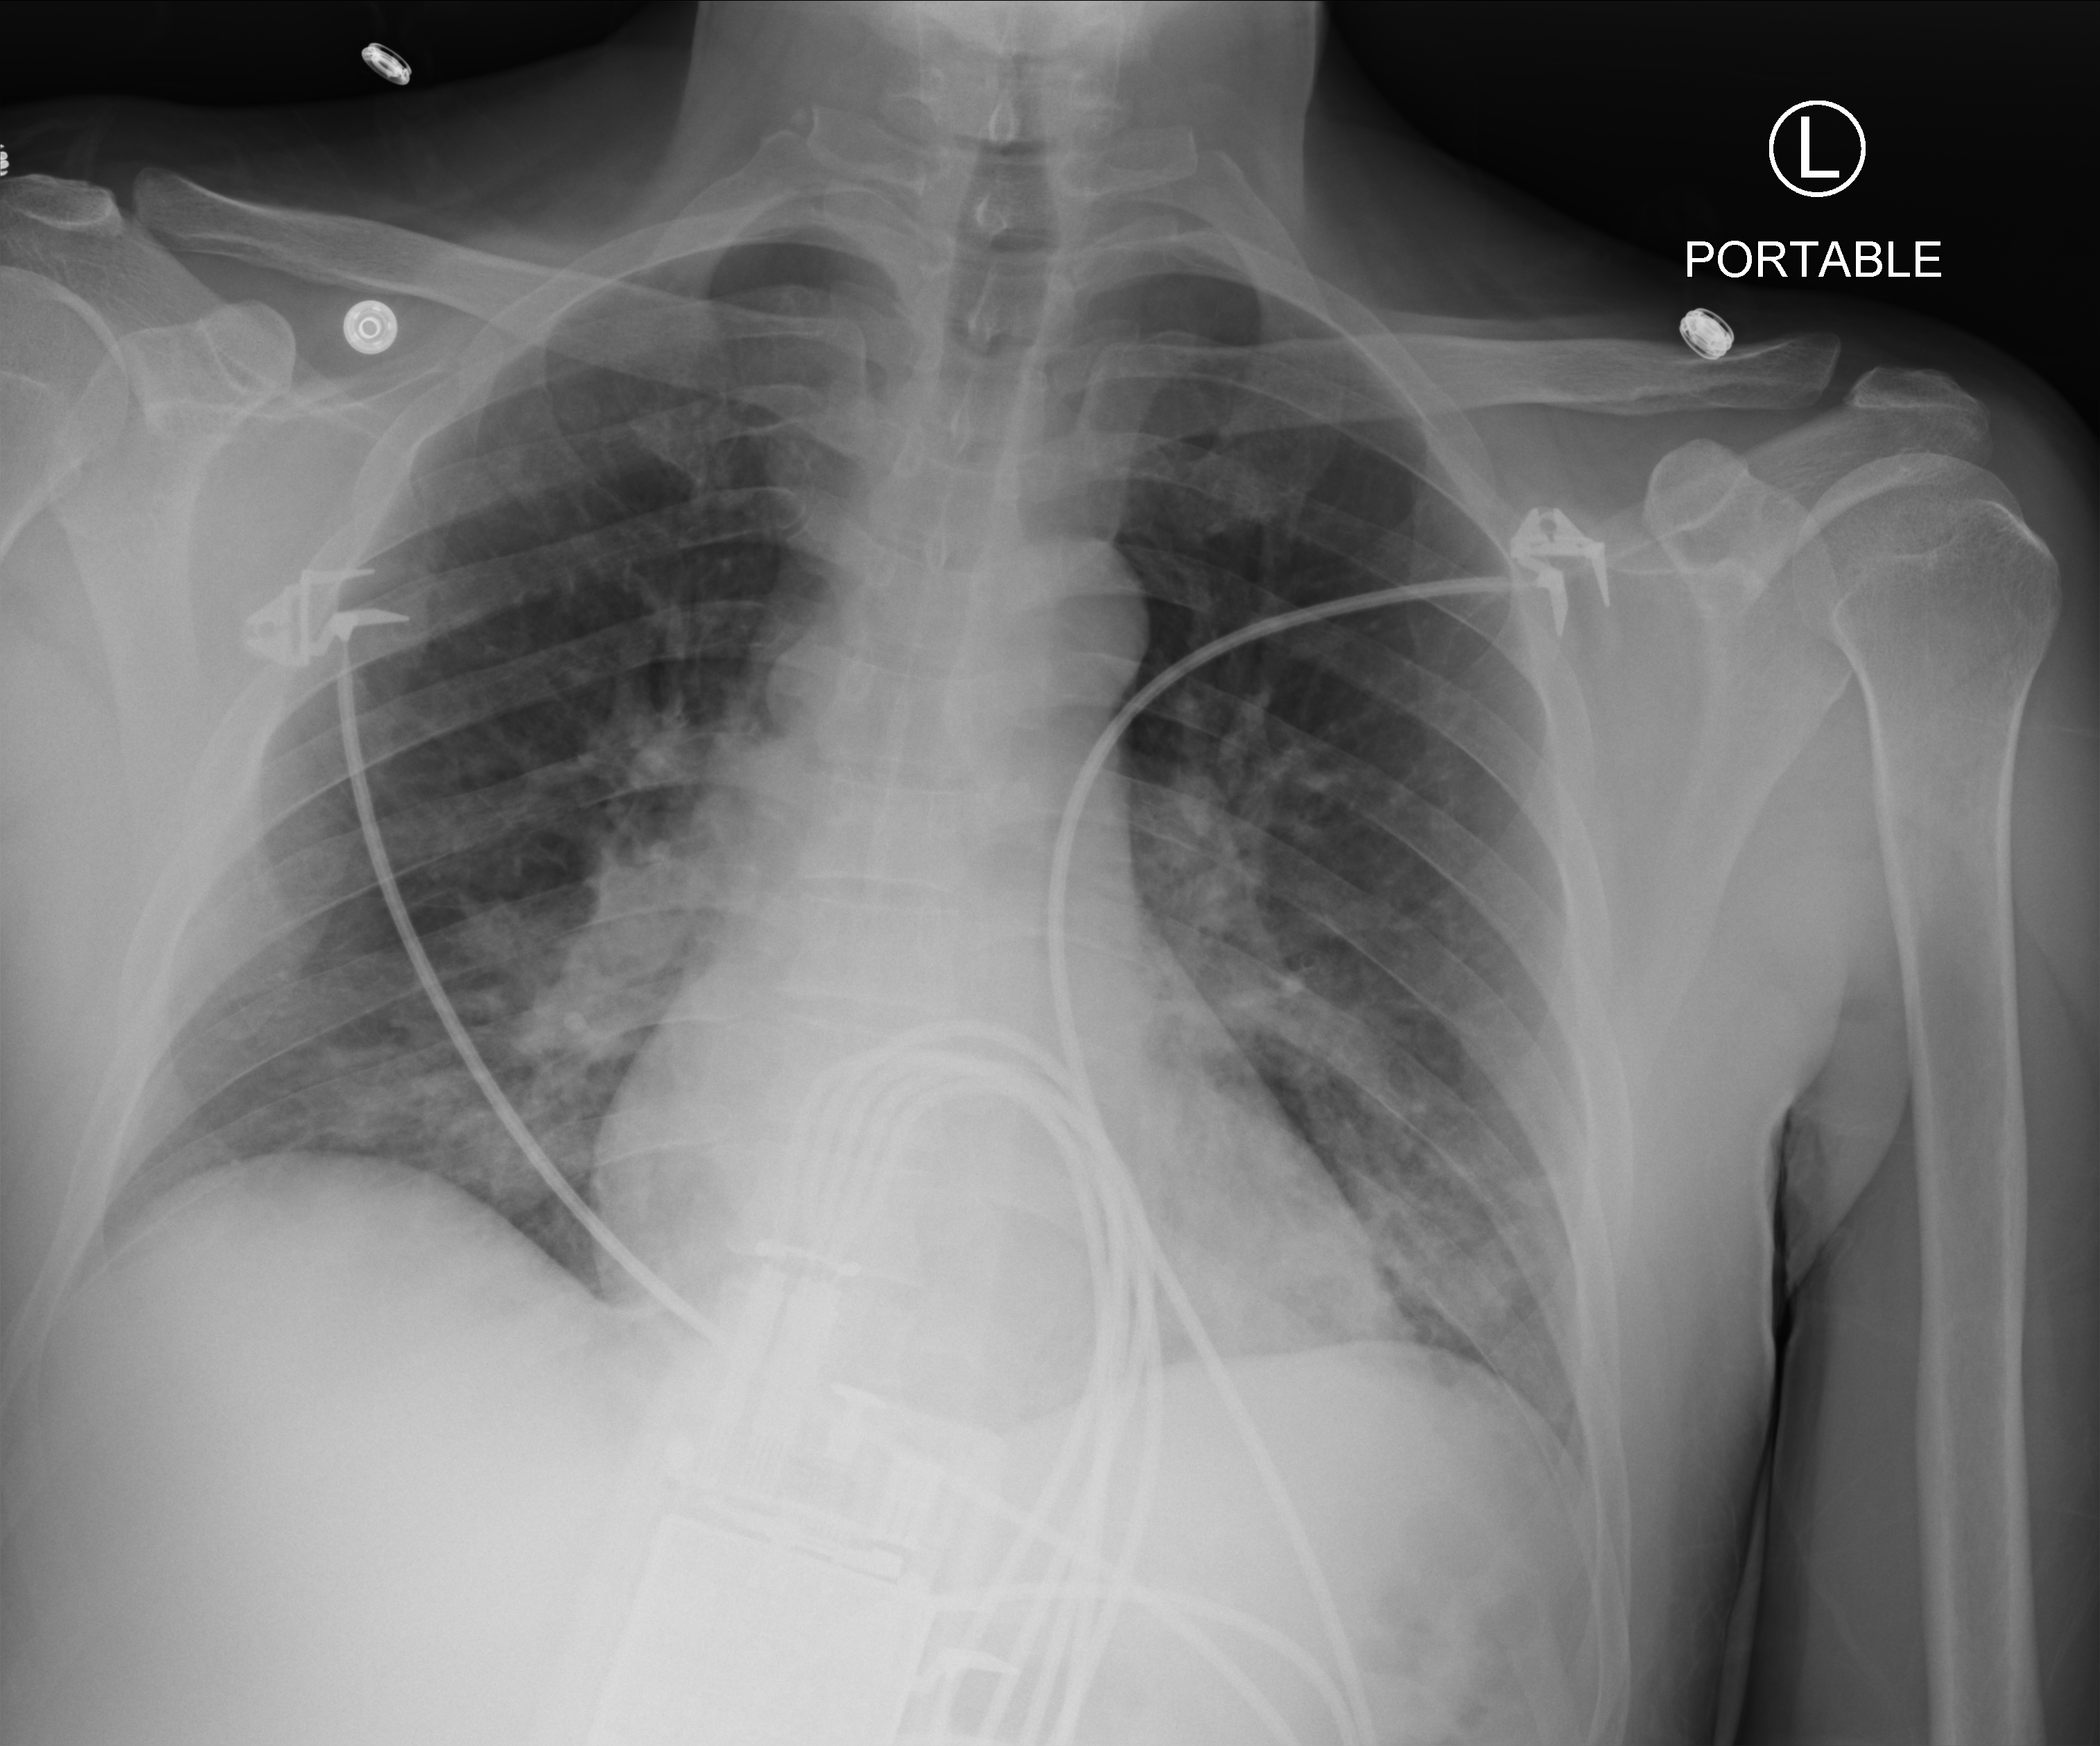
Bedside chest radiograph (computed radiography), anteroposterior (AP) projection. Male patient hospitalised with COVID-19, age 18–59 years.
Admission-level facts for this patient (not findings on this image; timing relative to this image not recorded): length of hospital stay: 11 days; mechanically ventilated during this hospital stay: no; admitted to intensive care during this hospital stay: no.